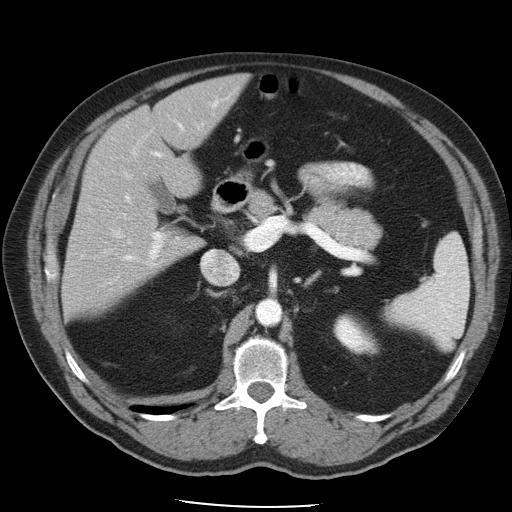
Contrast-enhanced abdominal CT, one axial slice. Position 28 of 49 along the scan axis. Reconstruction kernel STANDARD. Intravenous contrast given. Soft-tissue window (W 400 / L 40 HU). 5 mm slice thickness. 512 × 512 image matrix, field of view 395 × 395 mm. Male patient, age 68 years. Case-level facts recorded for this patient, not image findings: diagnosis: colorectal cancer liver metastases, imaged before liver resection; multiple liver metastases: yes; largest metastasis: 1.7 cm; chemotherapy before resection: yes.
Outlined on this slice (outlined manually by an expert reader):
- hepatic veins: bounding box (x1, y1, x2, y2) in pixels: (103, 171, 238, 282)
- liver: (64, 76, 245, 315)
- planned liver remnant (the part of the liver to remain after resection): (64, 76, 245, 315)
- portal vein (with intrahepatic branches): (81, 92, 235, 267)